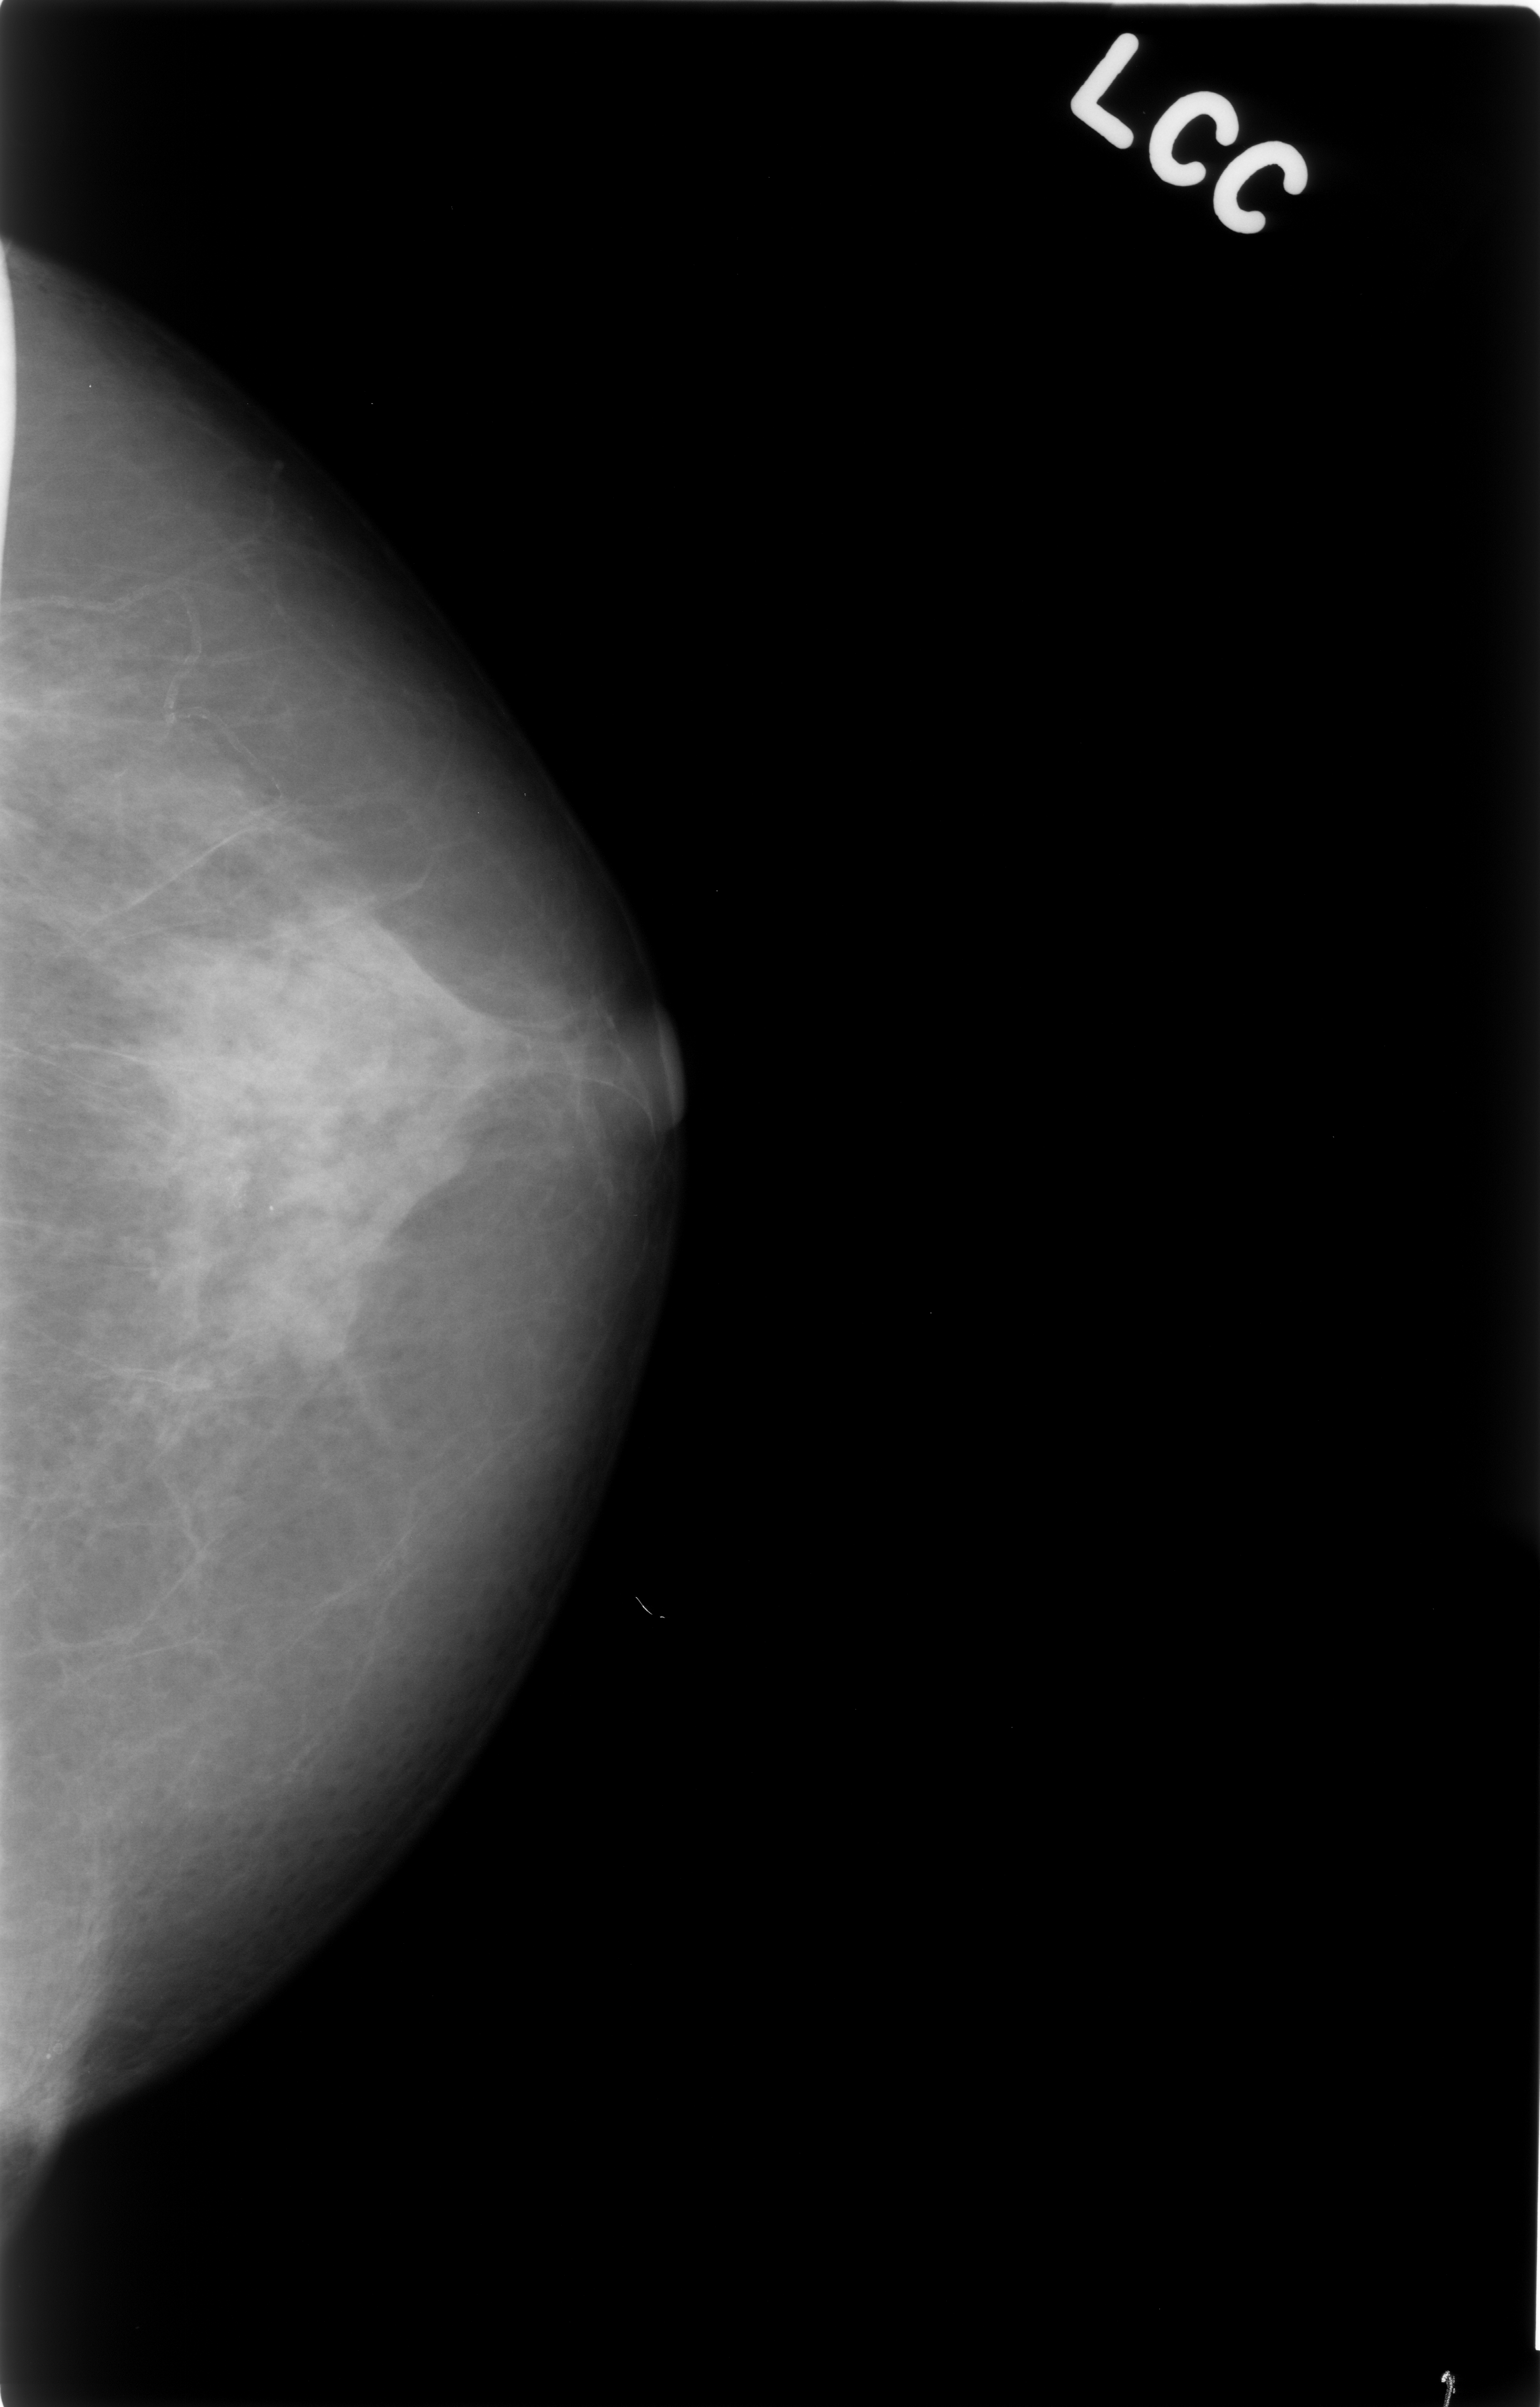
Mammogram (digitized film); left breast; craniocaudal (CC) view; breast composition: scattered fibroglandular densities (BI-RADS density category 2 of 4).
Finding: calcifications, morphology amorphous, distribution clustered; BI-RADS assessment category 4; pathology (as recorded): benign.